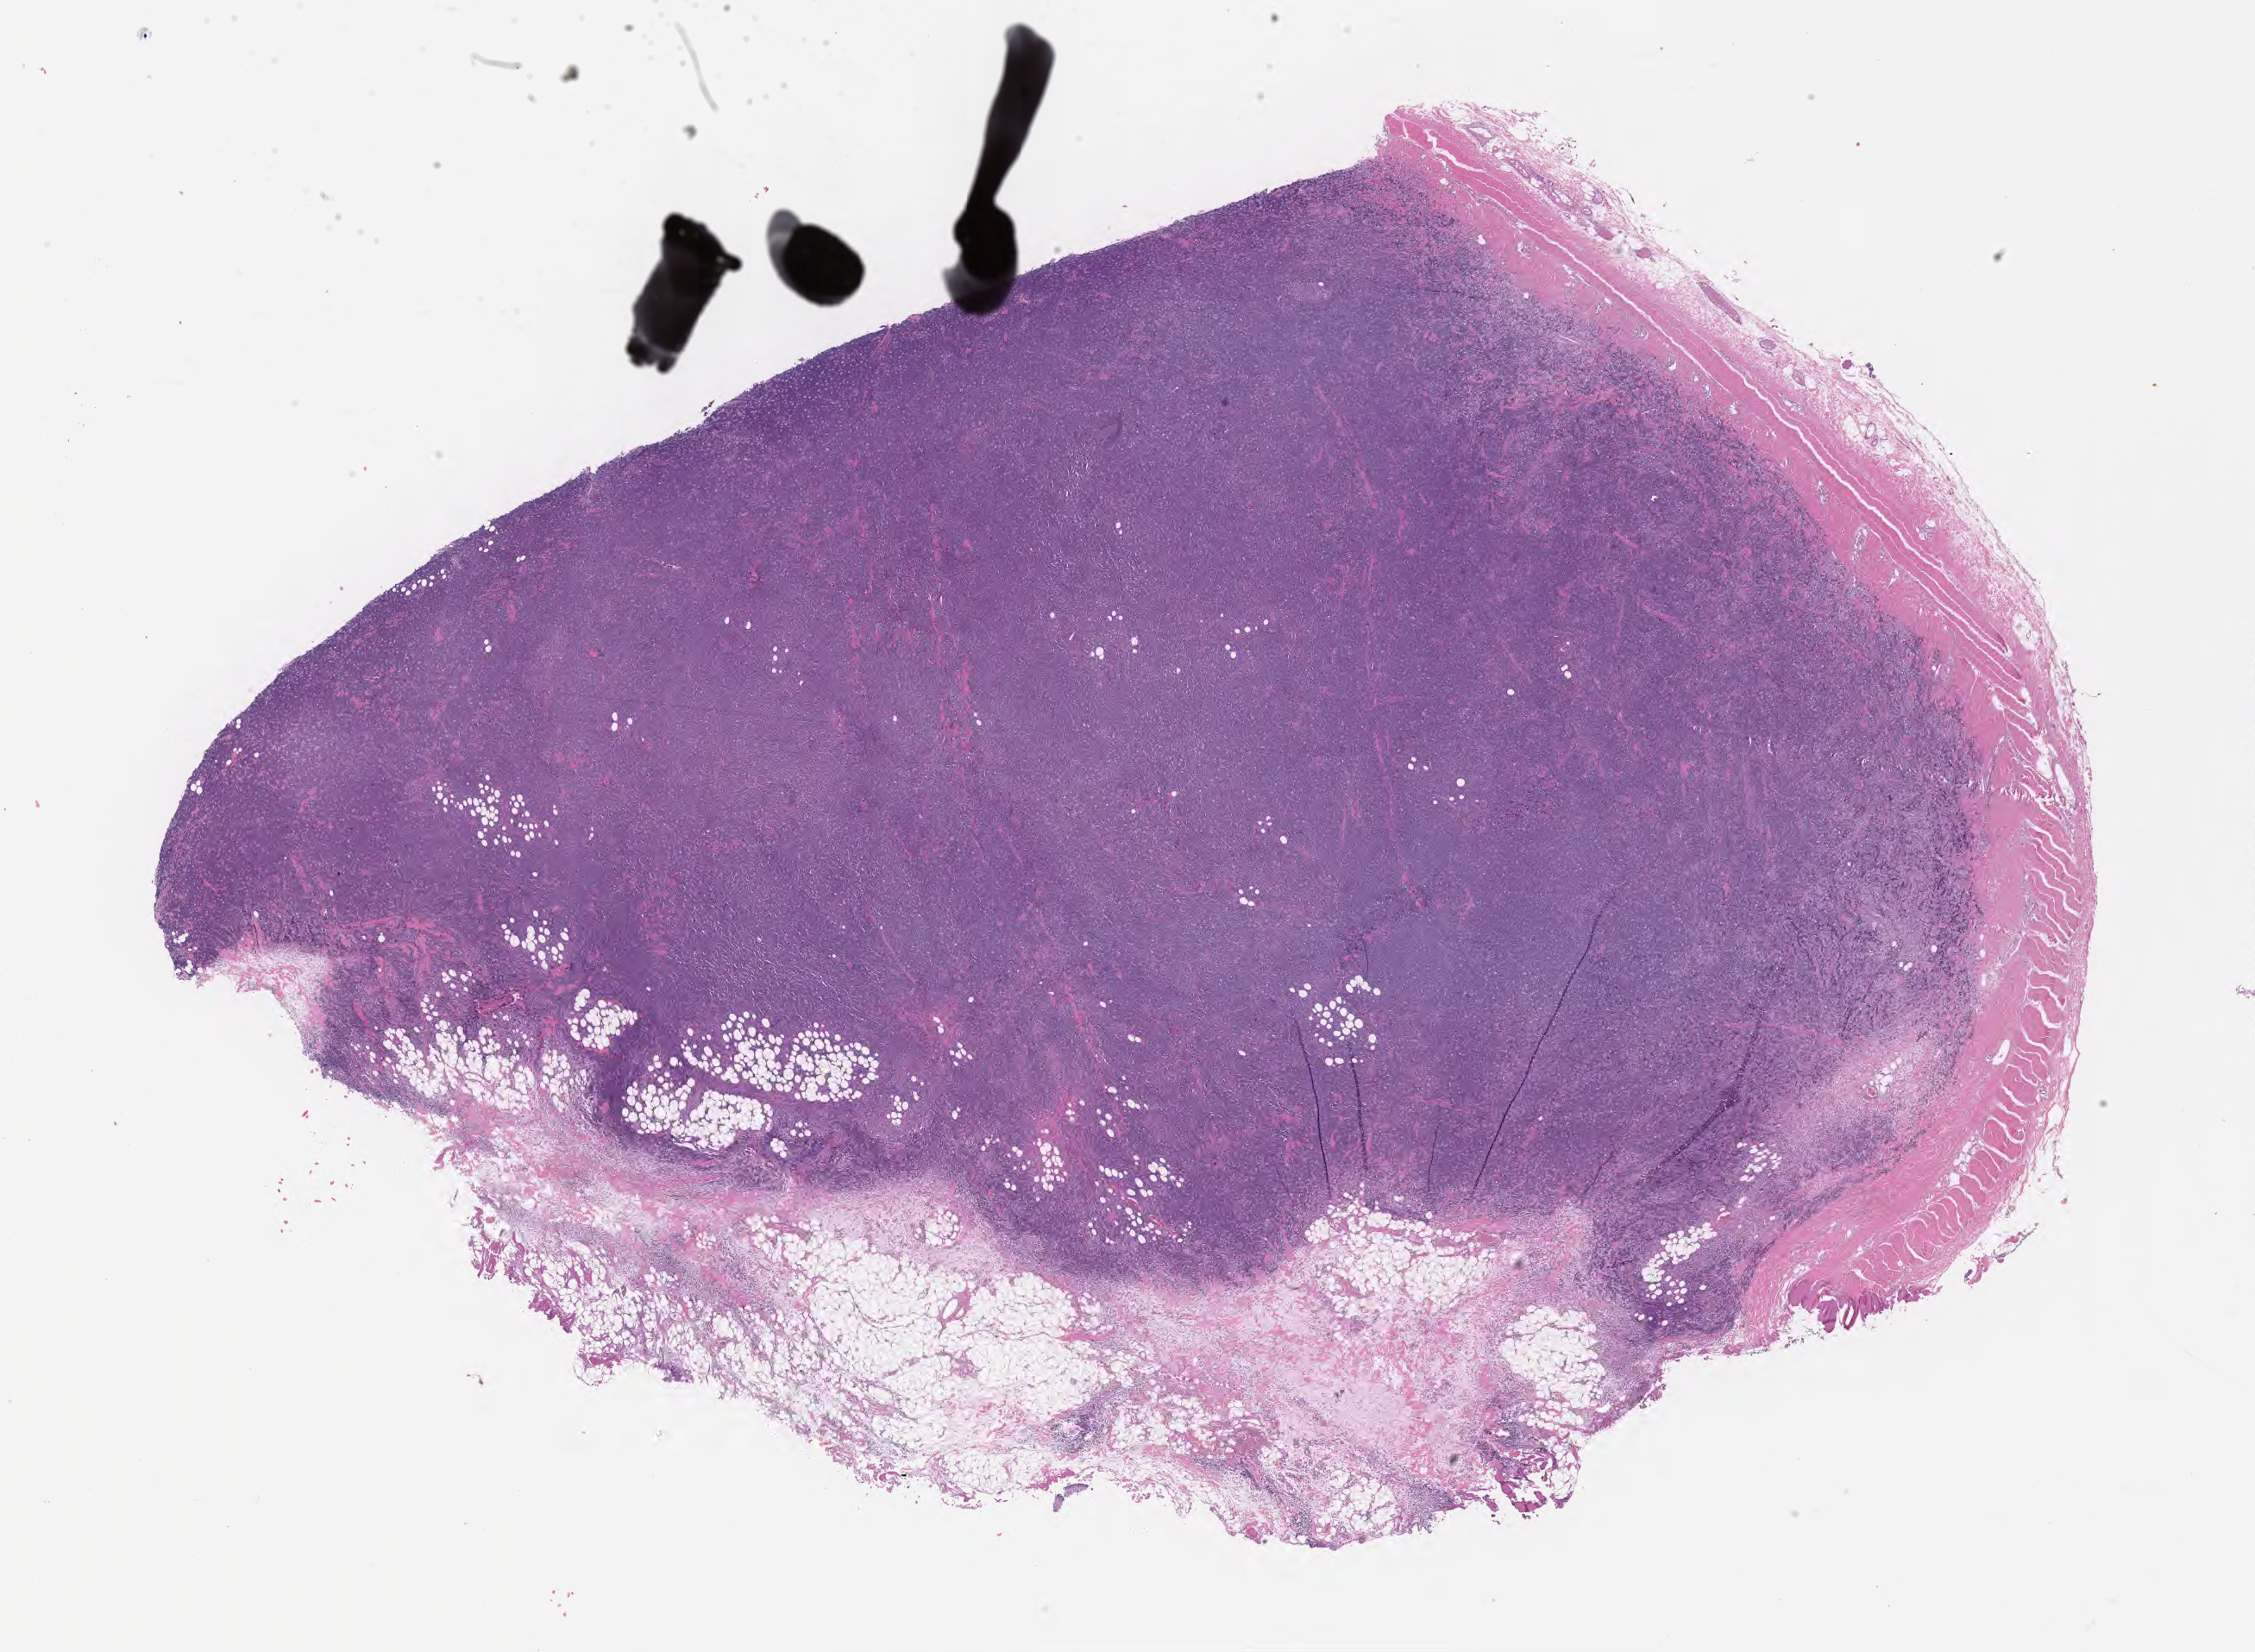
Digitized haematoxylin and eosin-stained section — shown as a low-resolution overview of the whole scanned area (about 21.1 x 15.5 mm), specimen: tumor tissue. Male patient; age at initial diagnosis 8 years.
• diagnosis: Burkitt lymphoma, NOS